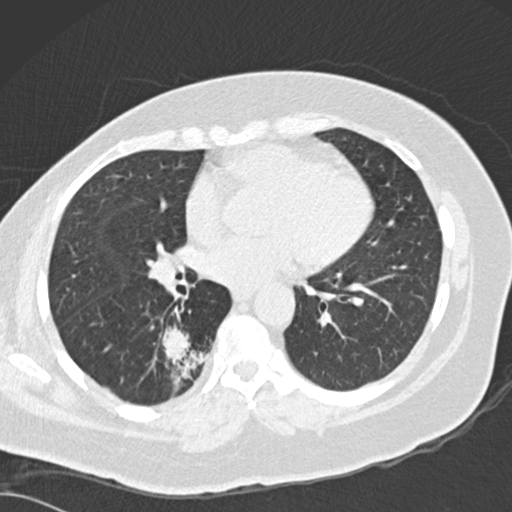
Low-dose screening chest CT, one axial slice. Slice 73 of 162 in the series (ordered by position). Reconstruction kernel B30f. Lung window (W 1500 / L -600 HU). 2 mm slice thickness. 512 × 512 image matrix.
Outlined on this slice (manually delineated by an expert):
- lesion 1 (tumor, lower lobe of right lung): bounding box (x1, y1, x2, y2) in pixels: (162, 325, 206, 392)